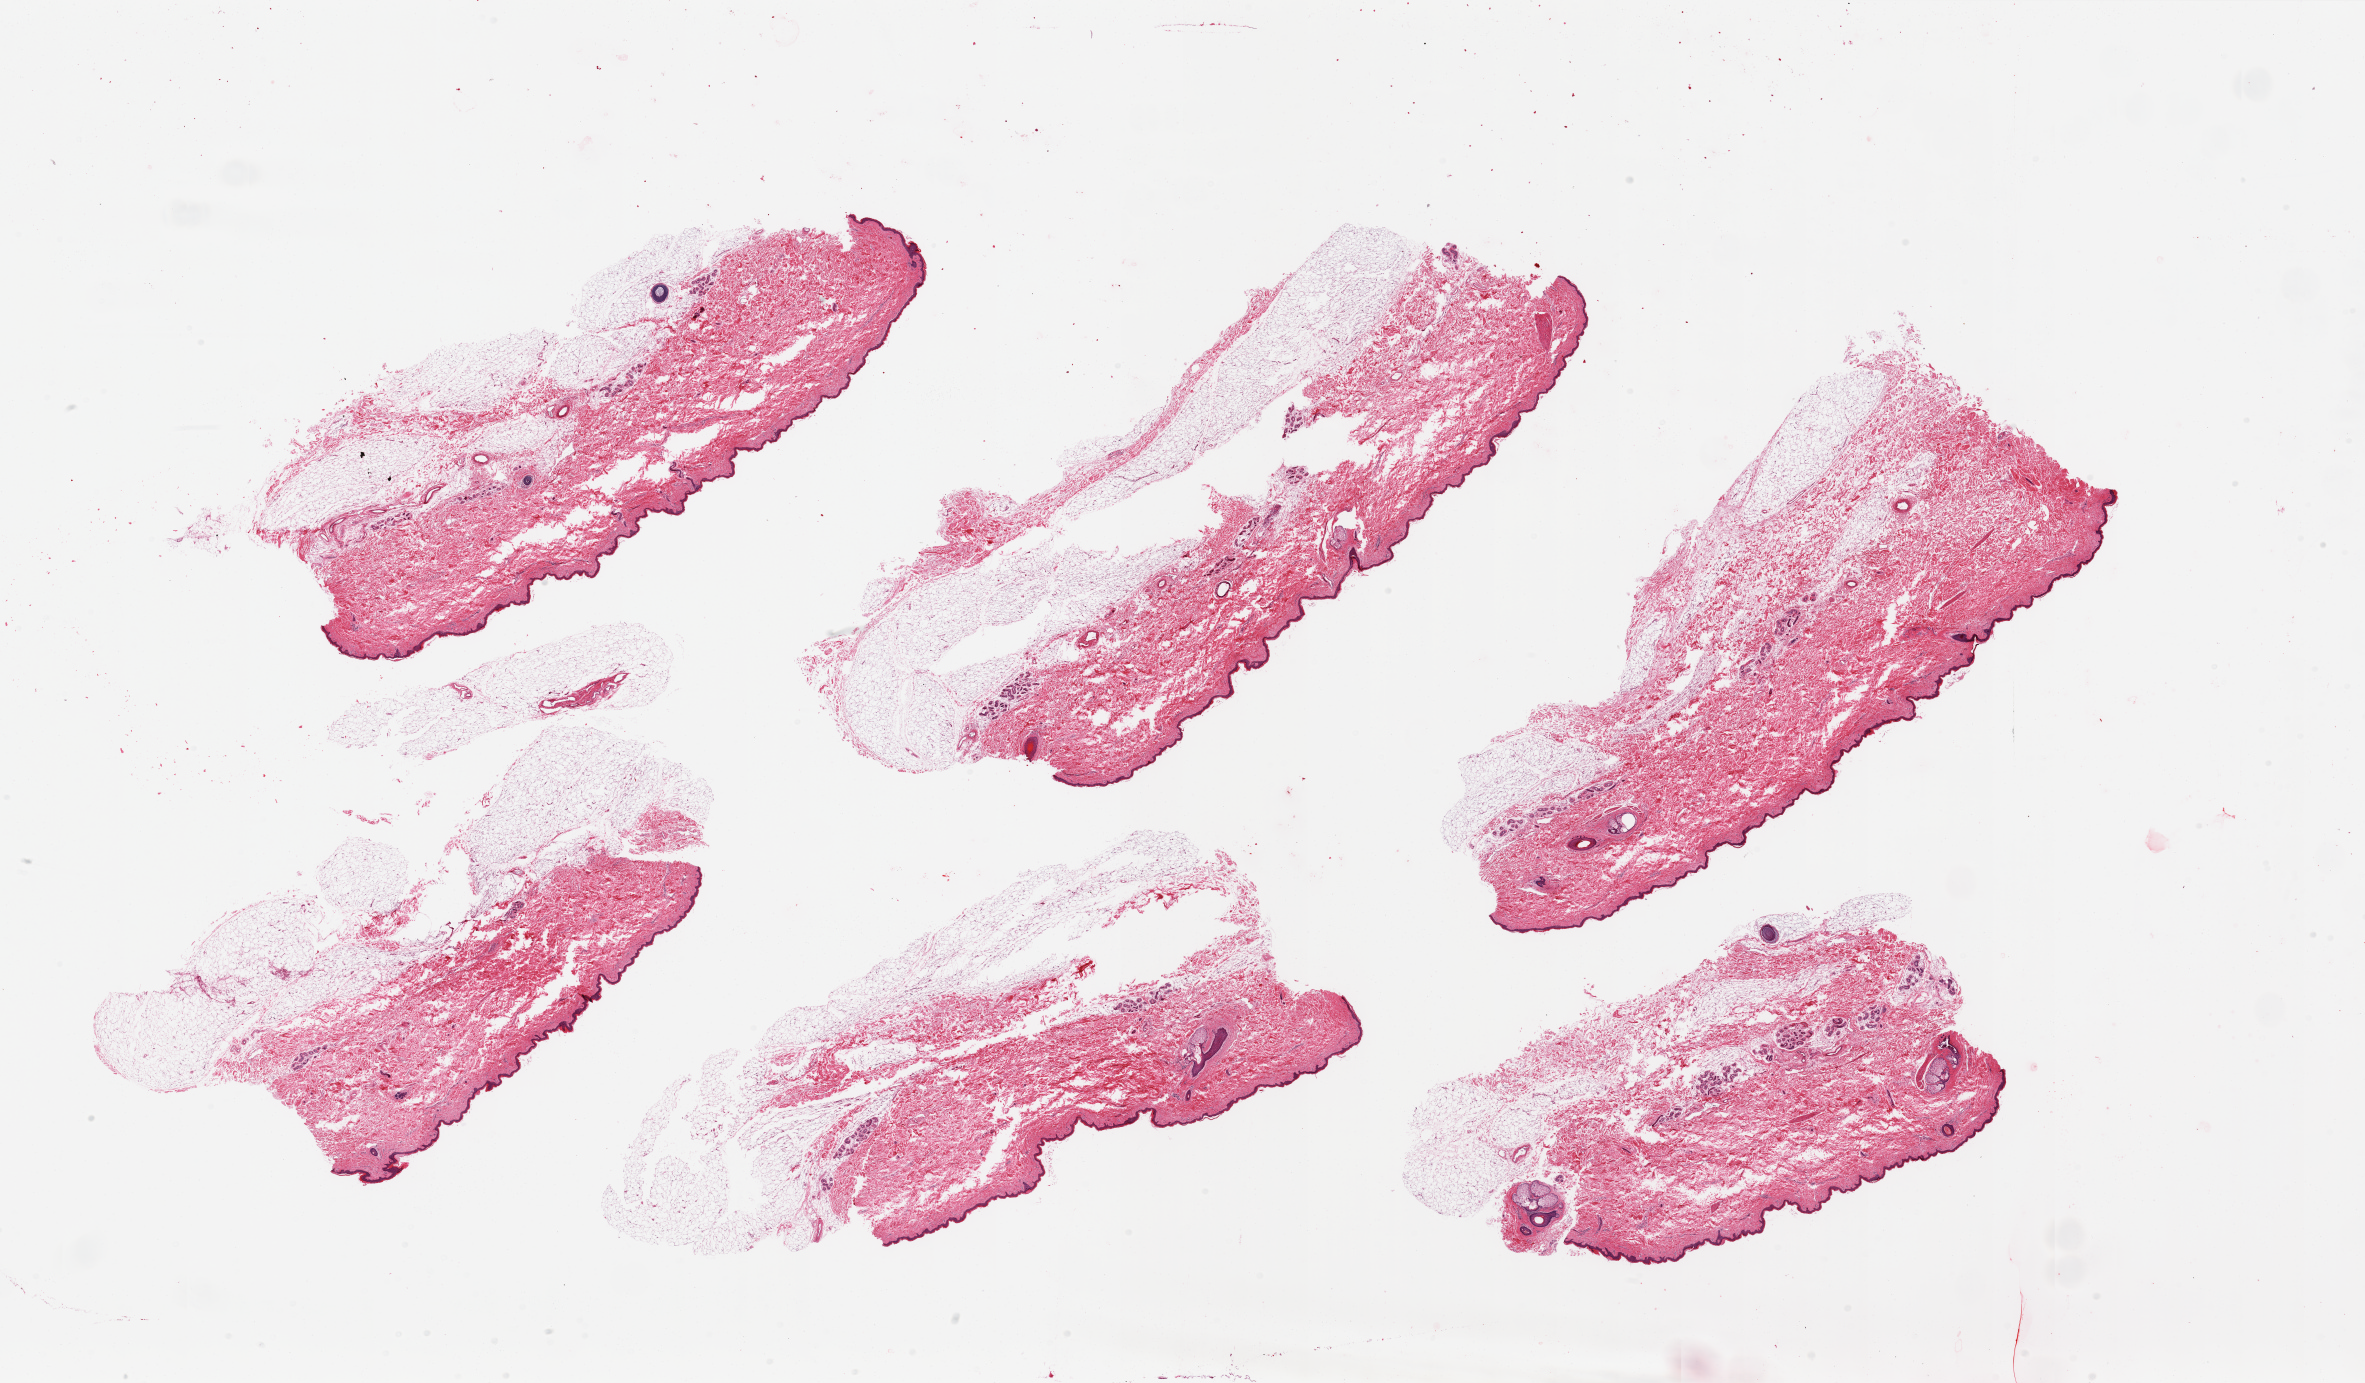
Digitized hematoxylin and eosin (H&E)-stained section, low-resolution overview of the scanned area, about 37.4 x 21.9 mm (acquisition: 20x scan); PAXgene-fixed, paraffin-embedded tissue; section of skin of suprapubic region (target tissue); tissue donor sample. Donor: male.
Review note (as recorded): 6 pieces; hair bearing skin with ~50% external fat.